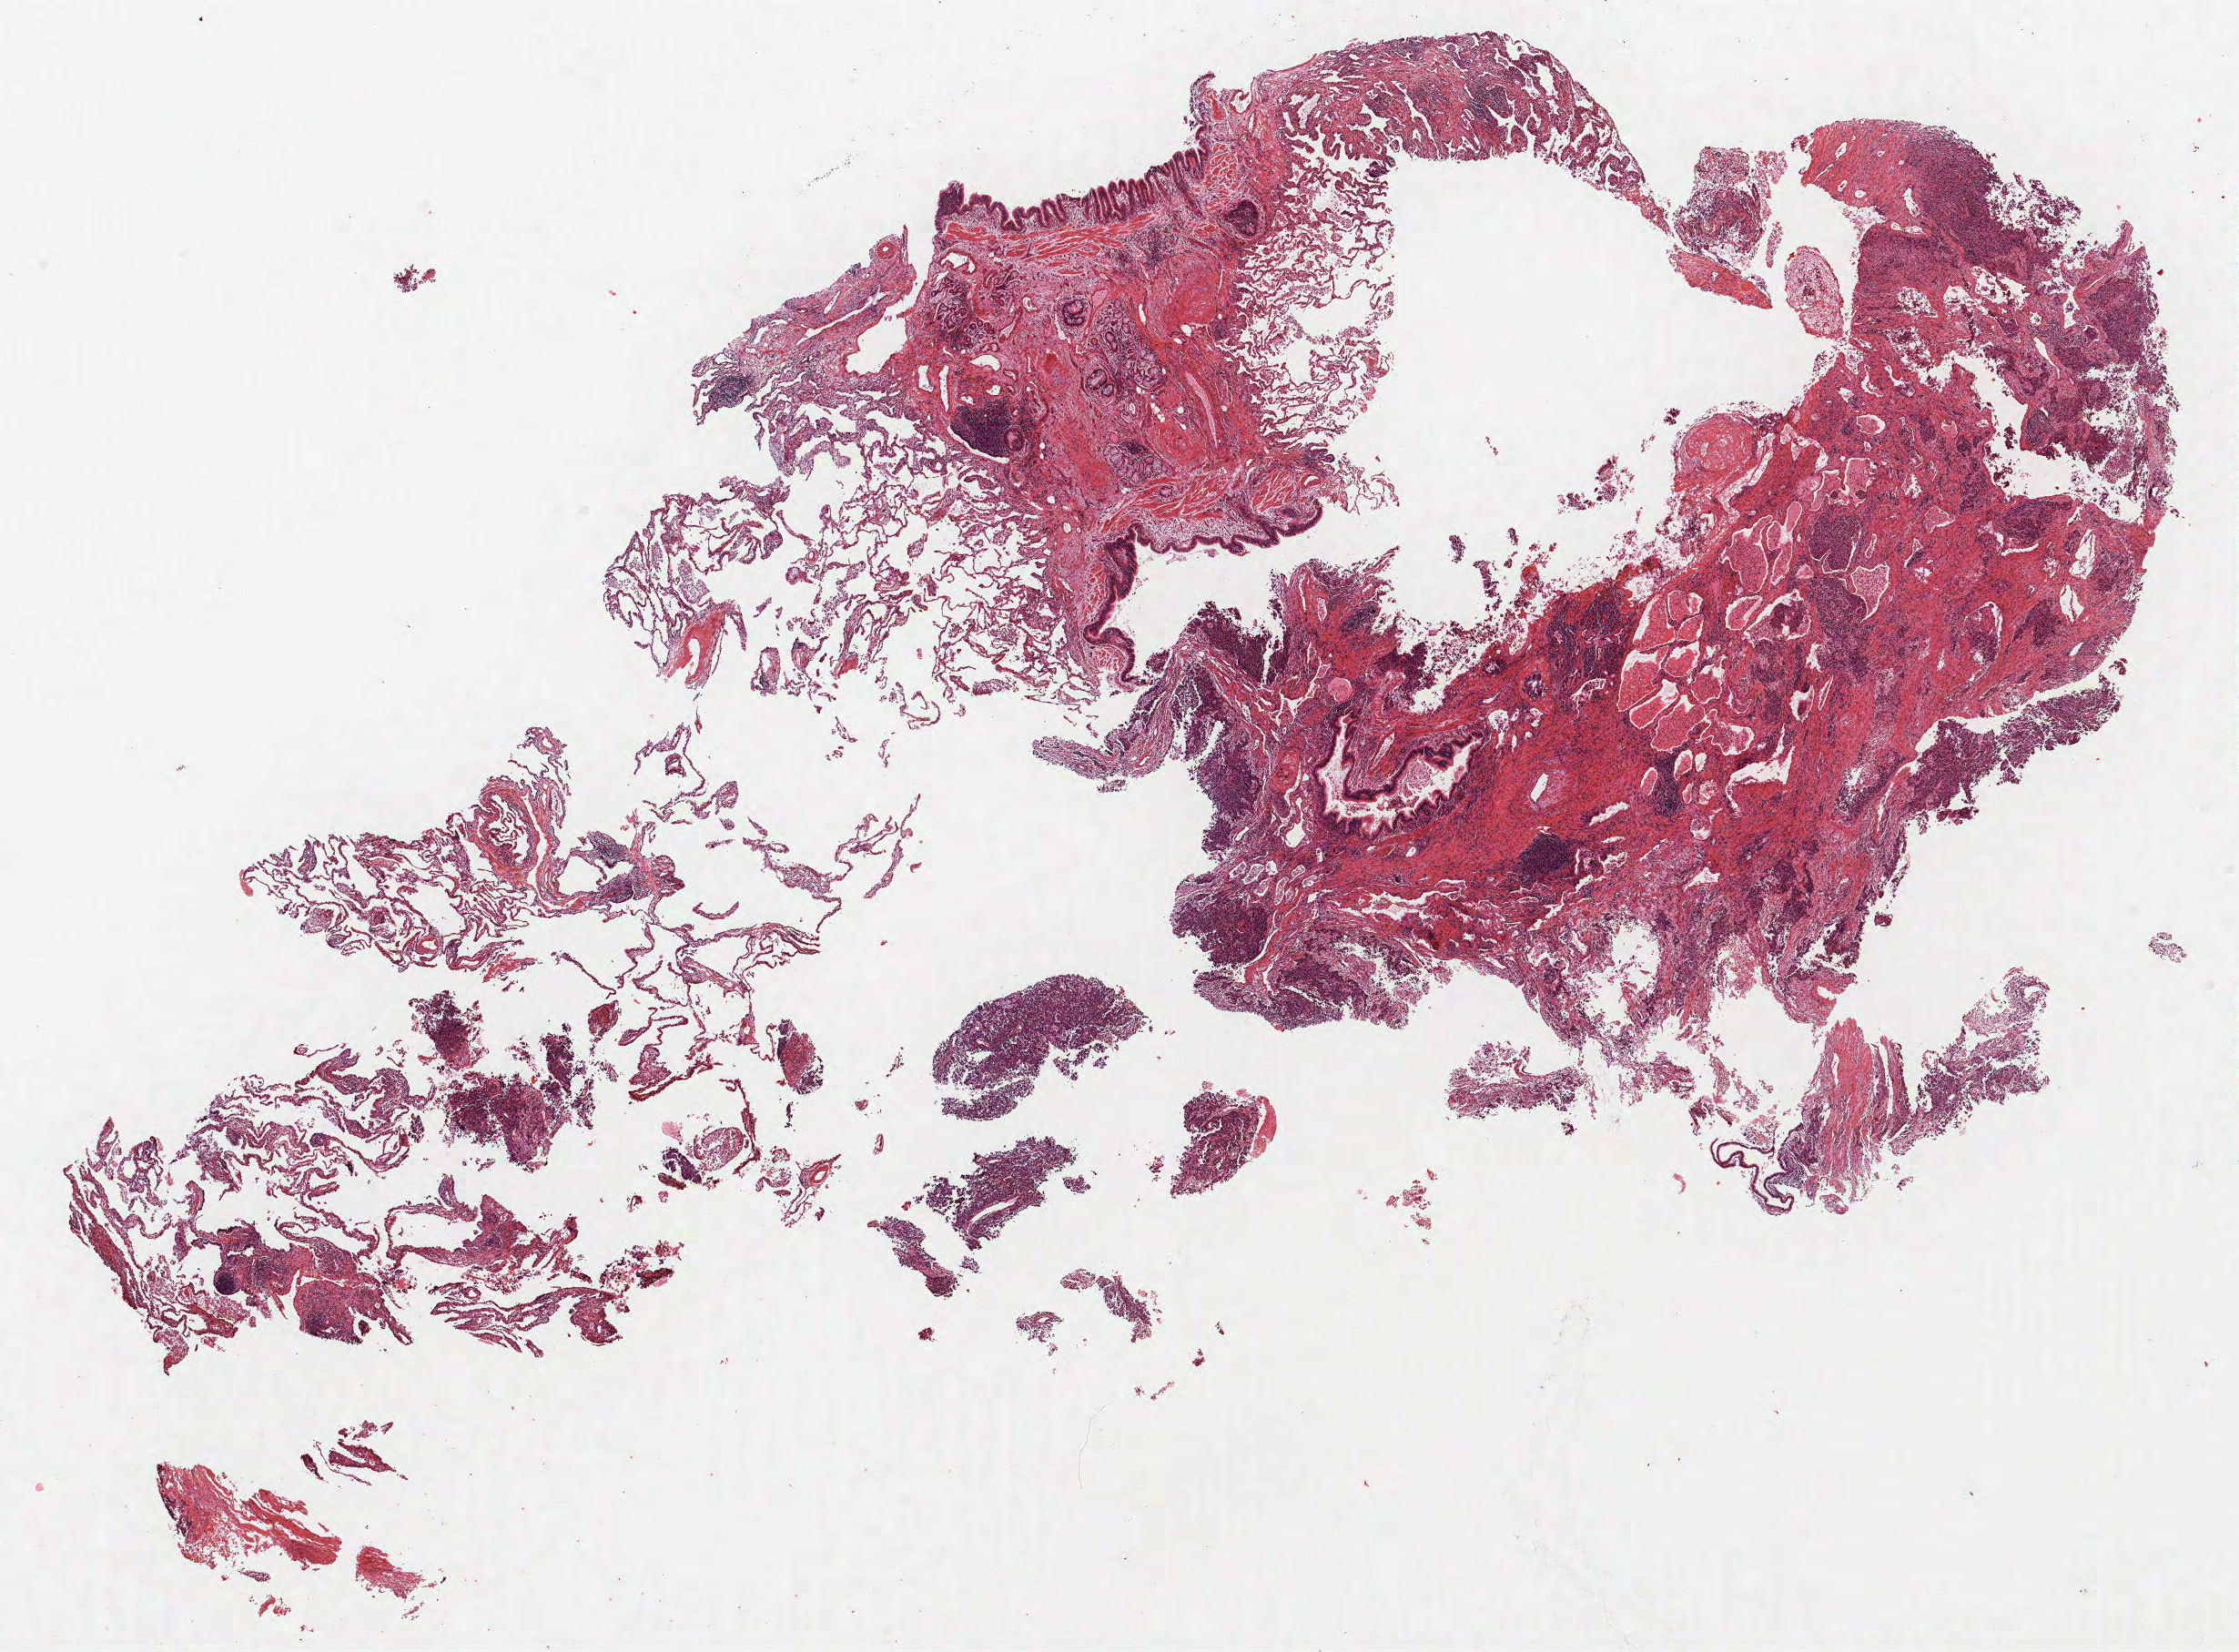
H&E whole-slide image, a low-resolution overview of the entire scanned area, about 19.7 x 14.5 mm (slide scanned at 40x), FFPE section, lung tissue. Male patient, aged 67 at enrolment. Former smoker at enrolment. Grade: poorly differentiated (G3).
* tumour size (pathology): 80 mm
* ICD-O-3 topography: lower lobe of lung (C34.3)
* participant's lung-cancer diagnosis: Adenocarcinoma, NOS (ICD-O-3 8140/3)
* stage (AJCC 6th edition): IB
* primary tumour location (clinical record): left lower lobe